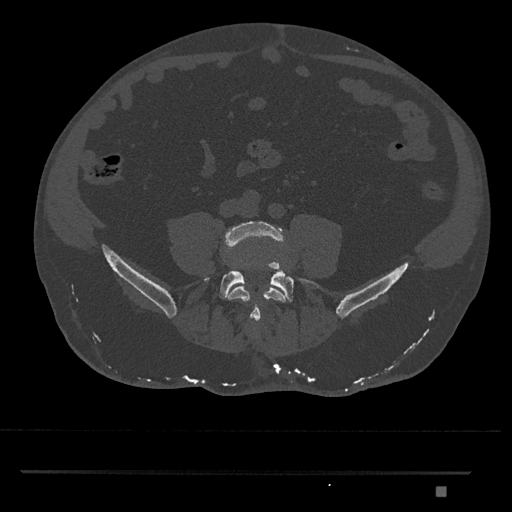
CT including the spine, one axial slice; position 581 of 1134 along the scan axis; 120 kVp; bone window (W 1800 / L 400 HU); 0.5 mm slice thickness; 512 × 512 image matrix, field of view 429 × 429 mm. Patient: male, 65 years. Case-level facts recorded for this patient, not image findings: primary cancer: prostate.
Structures marked on this image (semi-automatically segmented with operator editing):
- L4 vertebra: box from (x=223, y=221) to (x=289, y=325) px
- L5 vertebra: (x=204, y=263)–(x=320, y=302)